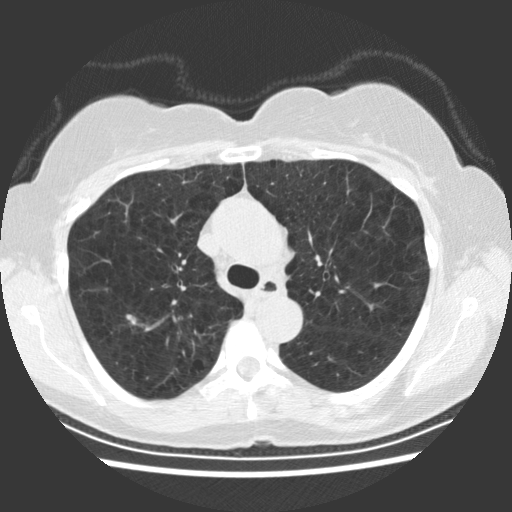
Low-dose screening chest CT, one axial slice. Lung window (W 1500 / L -600 HU). 512 × 512 image matrix, field of view 330 × 330 mm.
Structures marked on this image (manually delineated by an expert):
- lesion 1 (tumor, upper lobe of right lung): box from (x=126, y=314) to (x=136, y=325) px